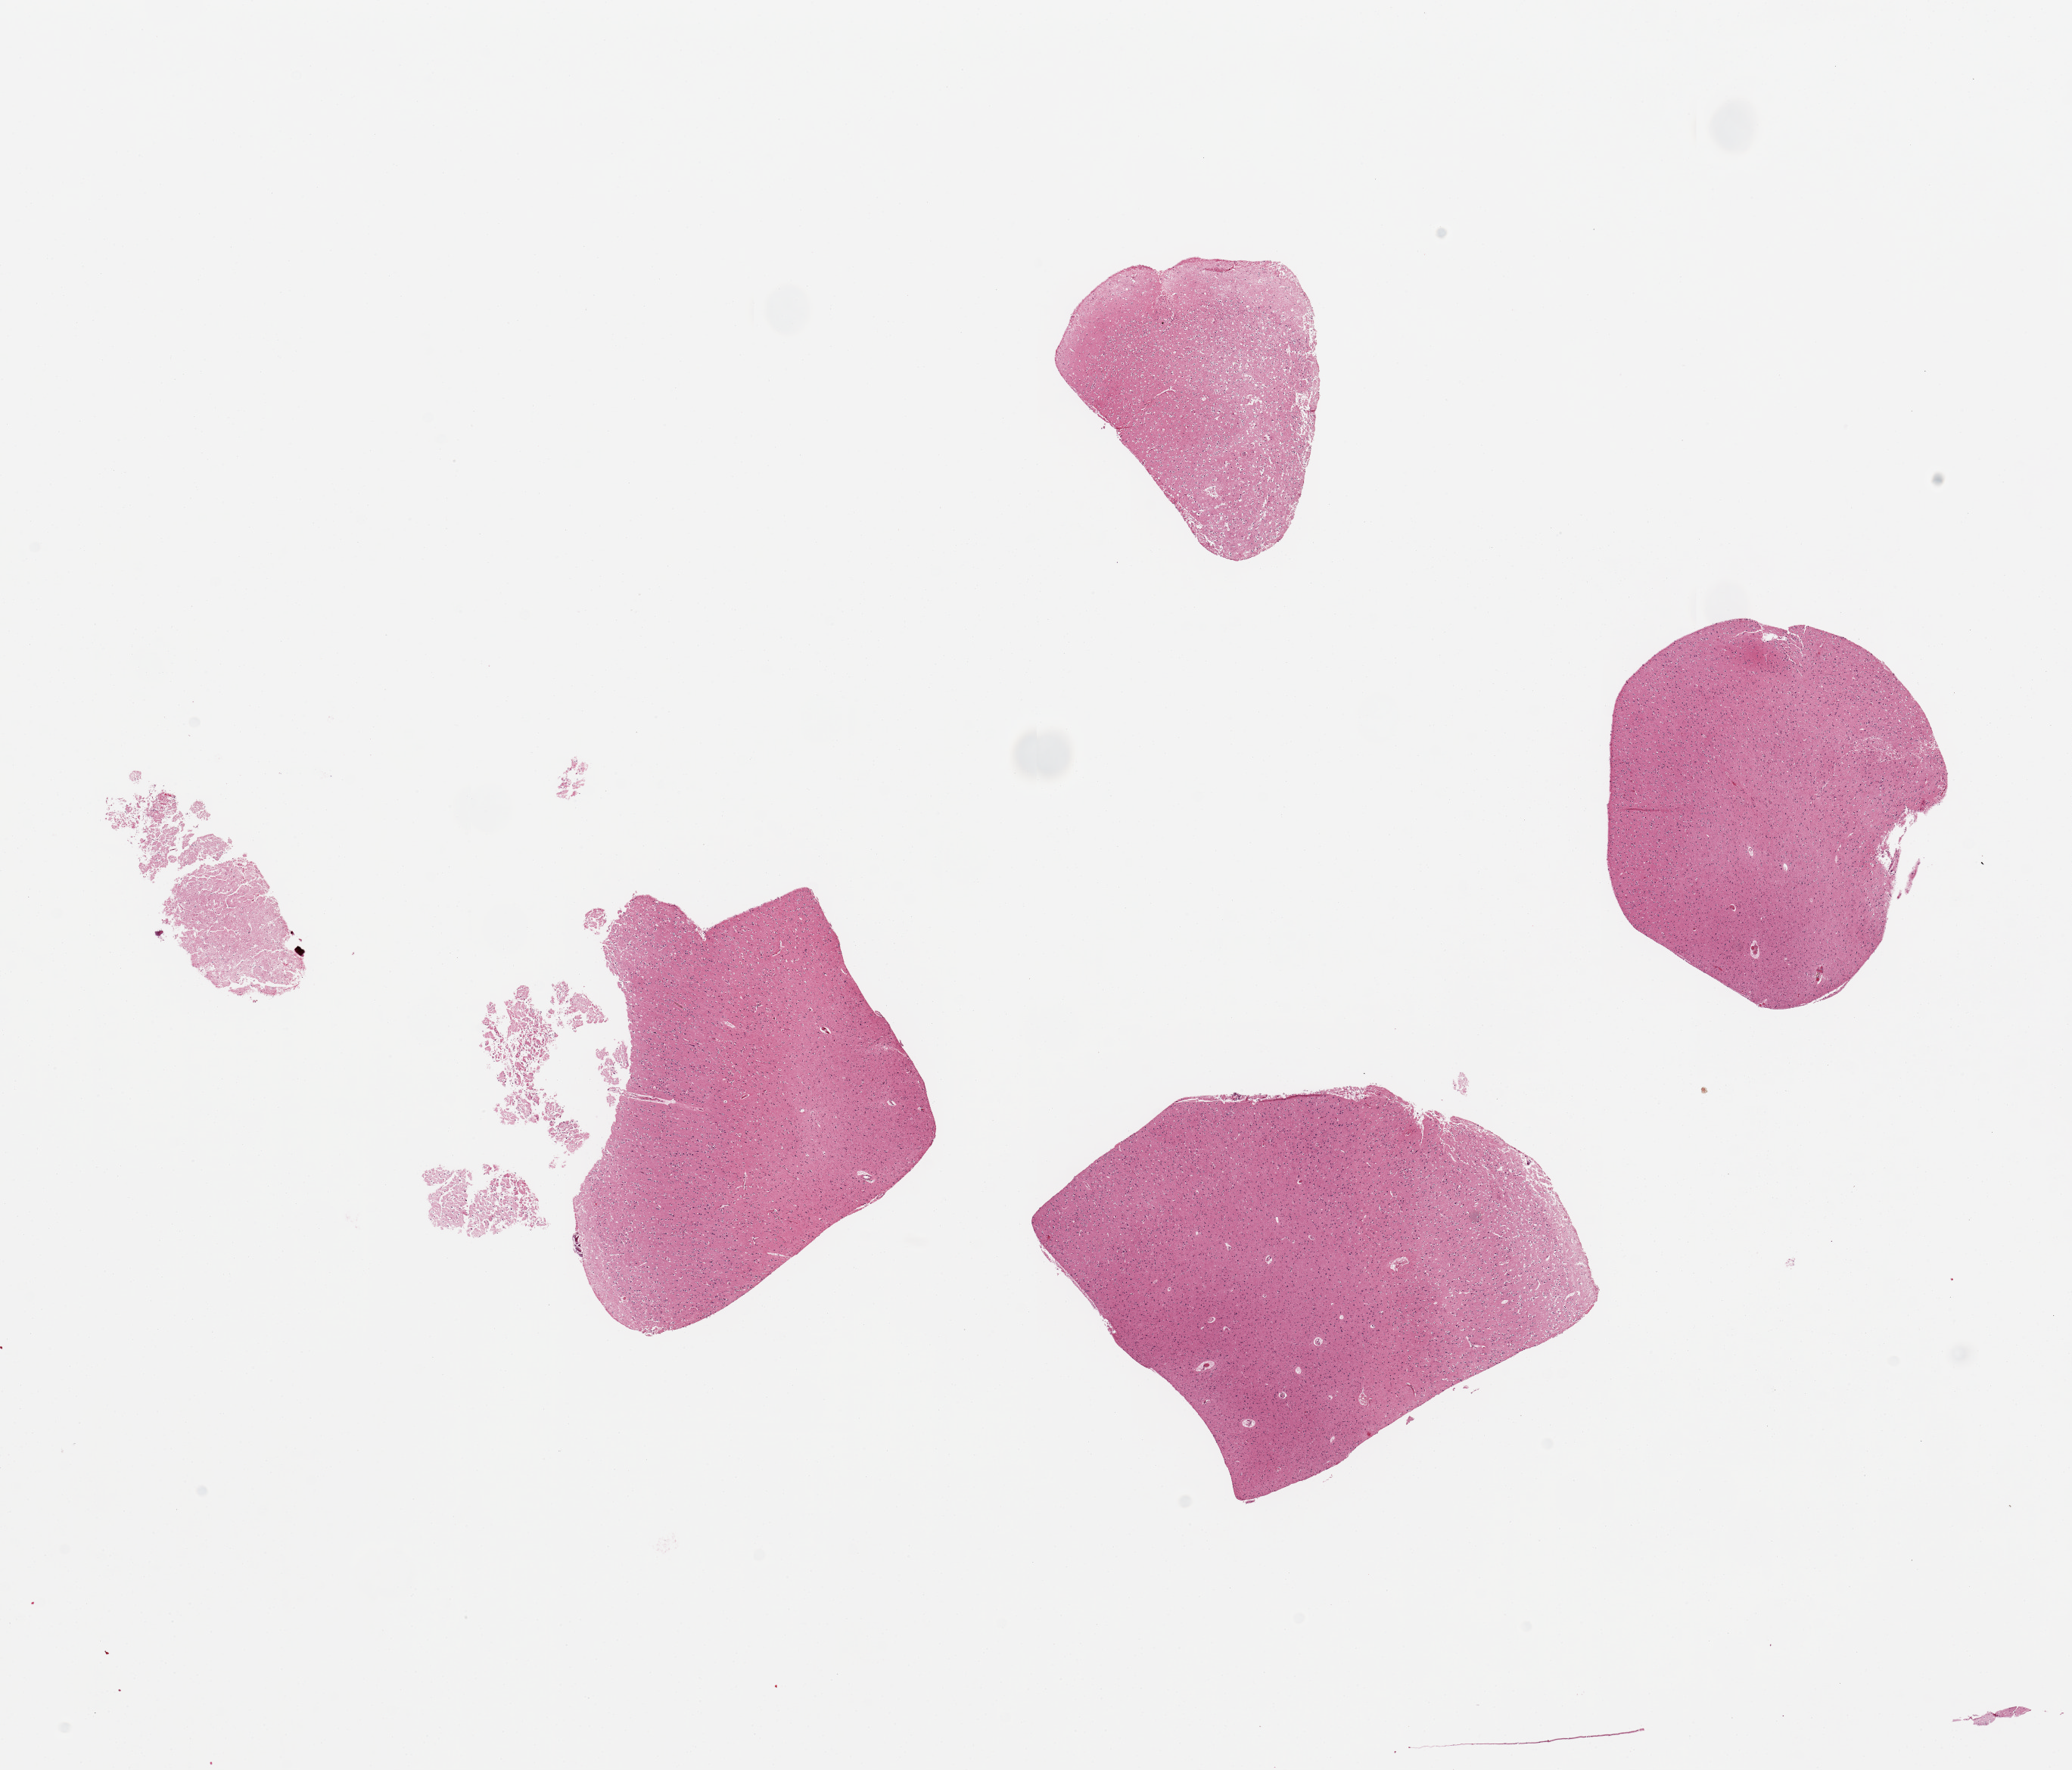
Digitized haematoxylin and eosin-stained section, shown as a low-resolution overview of the whole scanned area (about 21.7 x 18.5 mm, from a 20x scan); PAXgene-fixed, paraffin-embedded tissue; target tissue: cerebral cortex; donor tissue sample.
* pathologist's review note for this sample: 4 pieces